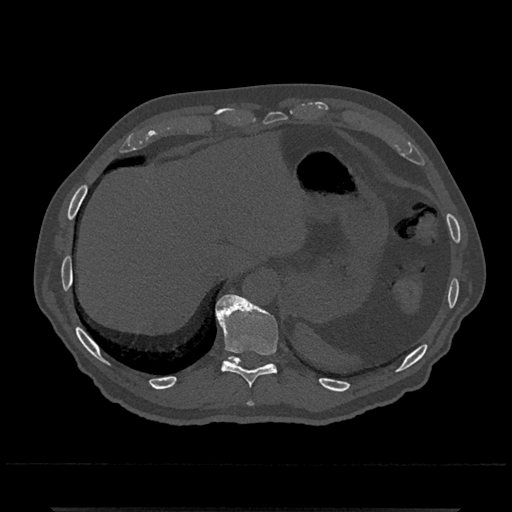
CT including the spine, one axial slice; slice 544 of 797 in the series (ordered by position); 120 kVp; bone window (W 1800 / L 400 HU); 512 × 512 image matrix, field of view 393 × 393 mm. Patient: male, 67 years. Case-level facts recorded for this patient, not image findings: primary cancer: prostate.
Outlined on this slice (semi-automatic segmentation, software-assisted and operator-edited):
- T10 vertebra: bounding box [x1, y1, x2, y2] px = [215, 294, 279, 387]
- T11 vertebra: [226, 356, 271, 366]
- T9 vertebra: [248, 402, 254, 406]